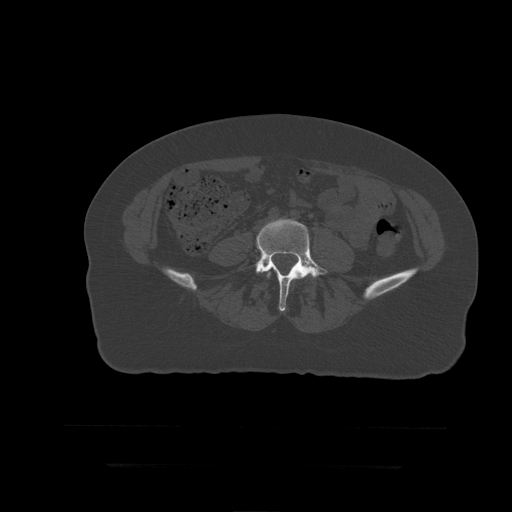
CT including the spine, one axial slice; position 78 of 399 along the scan axis; 120 kVp; bone window (W 1800 / L 400 HU); 1.25 mm slice thickness; 512 × 512 image matrix, field of view 450 × 450 mm. Patient age 41 years. From the clinical record (not read from this slice): primary cancer: breast.
Structures marked on this image (semi-automatically segmented with operator editing):
- L4 vertebra: bounding box (x1, y1, x2, y2) in pixels: (267, 264, 296, 278)
- L5 vertebra: (256, 219, 328, 312)